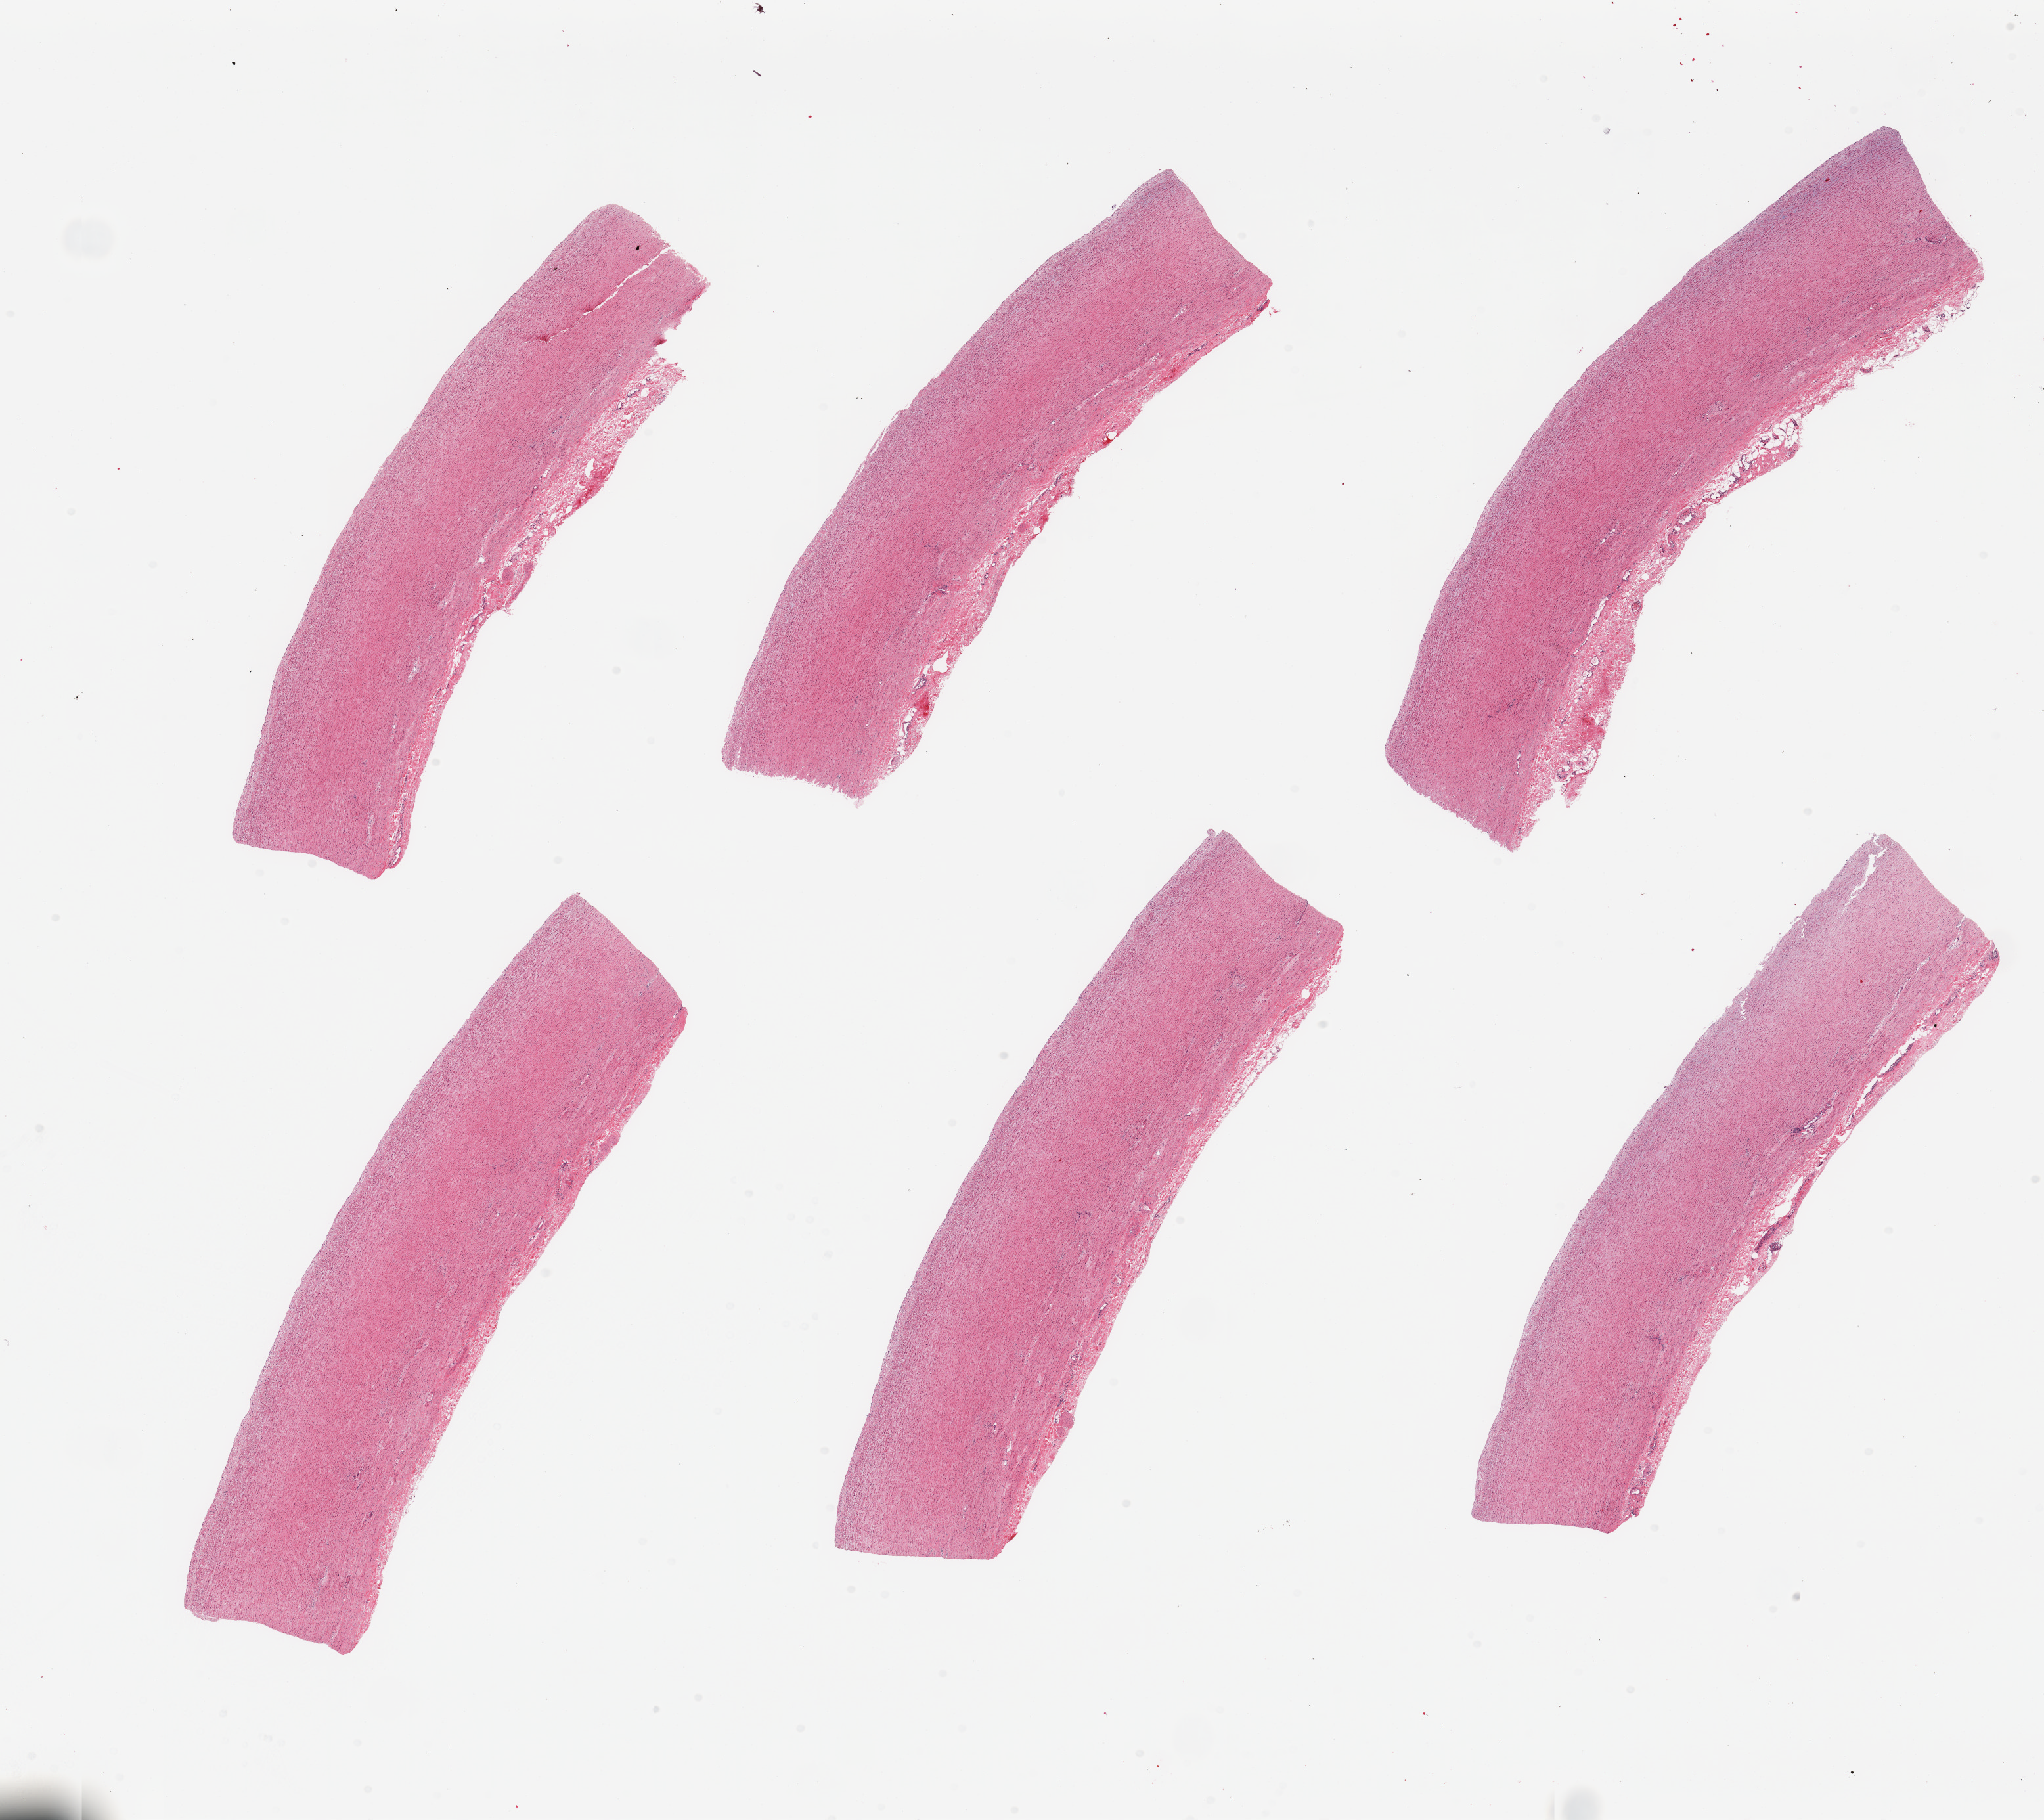
Haematoxylin and eosin whole-slide image, whole scanned area (about 24.6 x 21.9 mm) shown as a low-resolution overview, PAXgene-fixed, paraffin-embedded tissue, sampled site (target tissue): aorta, tissue donor sample. Male donor.
Pathologist's review note for this sample: 6 pieces, minimal atherosis.